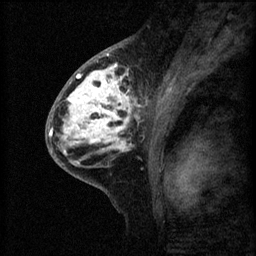
Breast MRI (dynamic contrast-enhanced), one sagittal slice; position 32 of 60 along the scan axis; 3 images stored at this slice position (order not interpretable as contrast timing); 1.5 T; TE 4.2 ms, TR 8.2 ms; 2 mm slice thickness; 256 × 256 image matrix, field of view 180 × 180 mm. Patient: female, 41 years.
Annotated regions visible in this slice (semi-automatically segmented with operator editing):
- analysis volume of interest (the breast-tissue region the enhancement analysis was run in; not a lesion): bounding box <53,62,160,175> (left, top, right, bottom; pixels)
- tumour enhancement mask (voxels above the 70 % enhancement threshold inside the analysis volume of interest): <63,62,143,155>